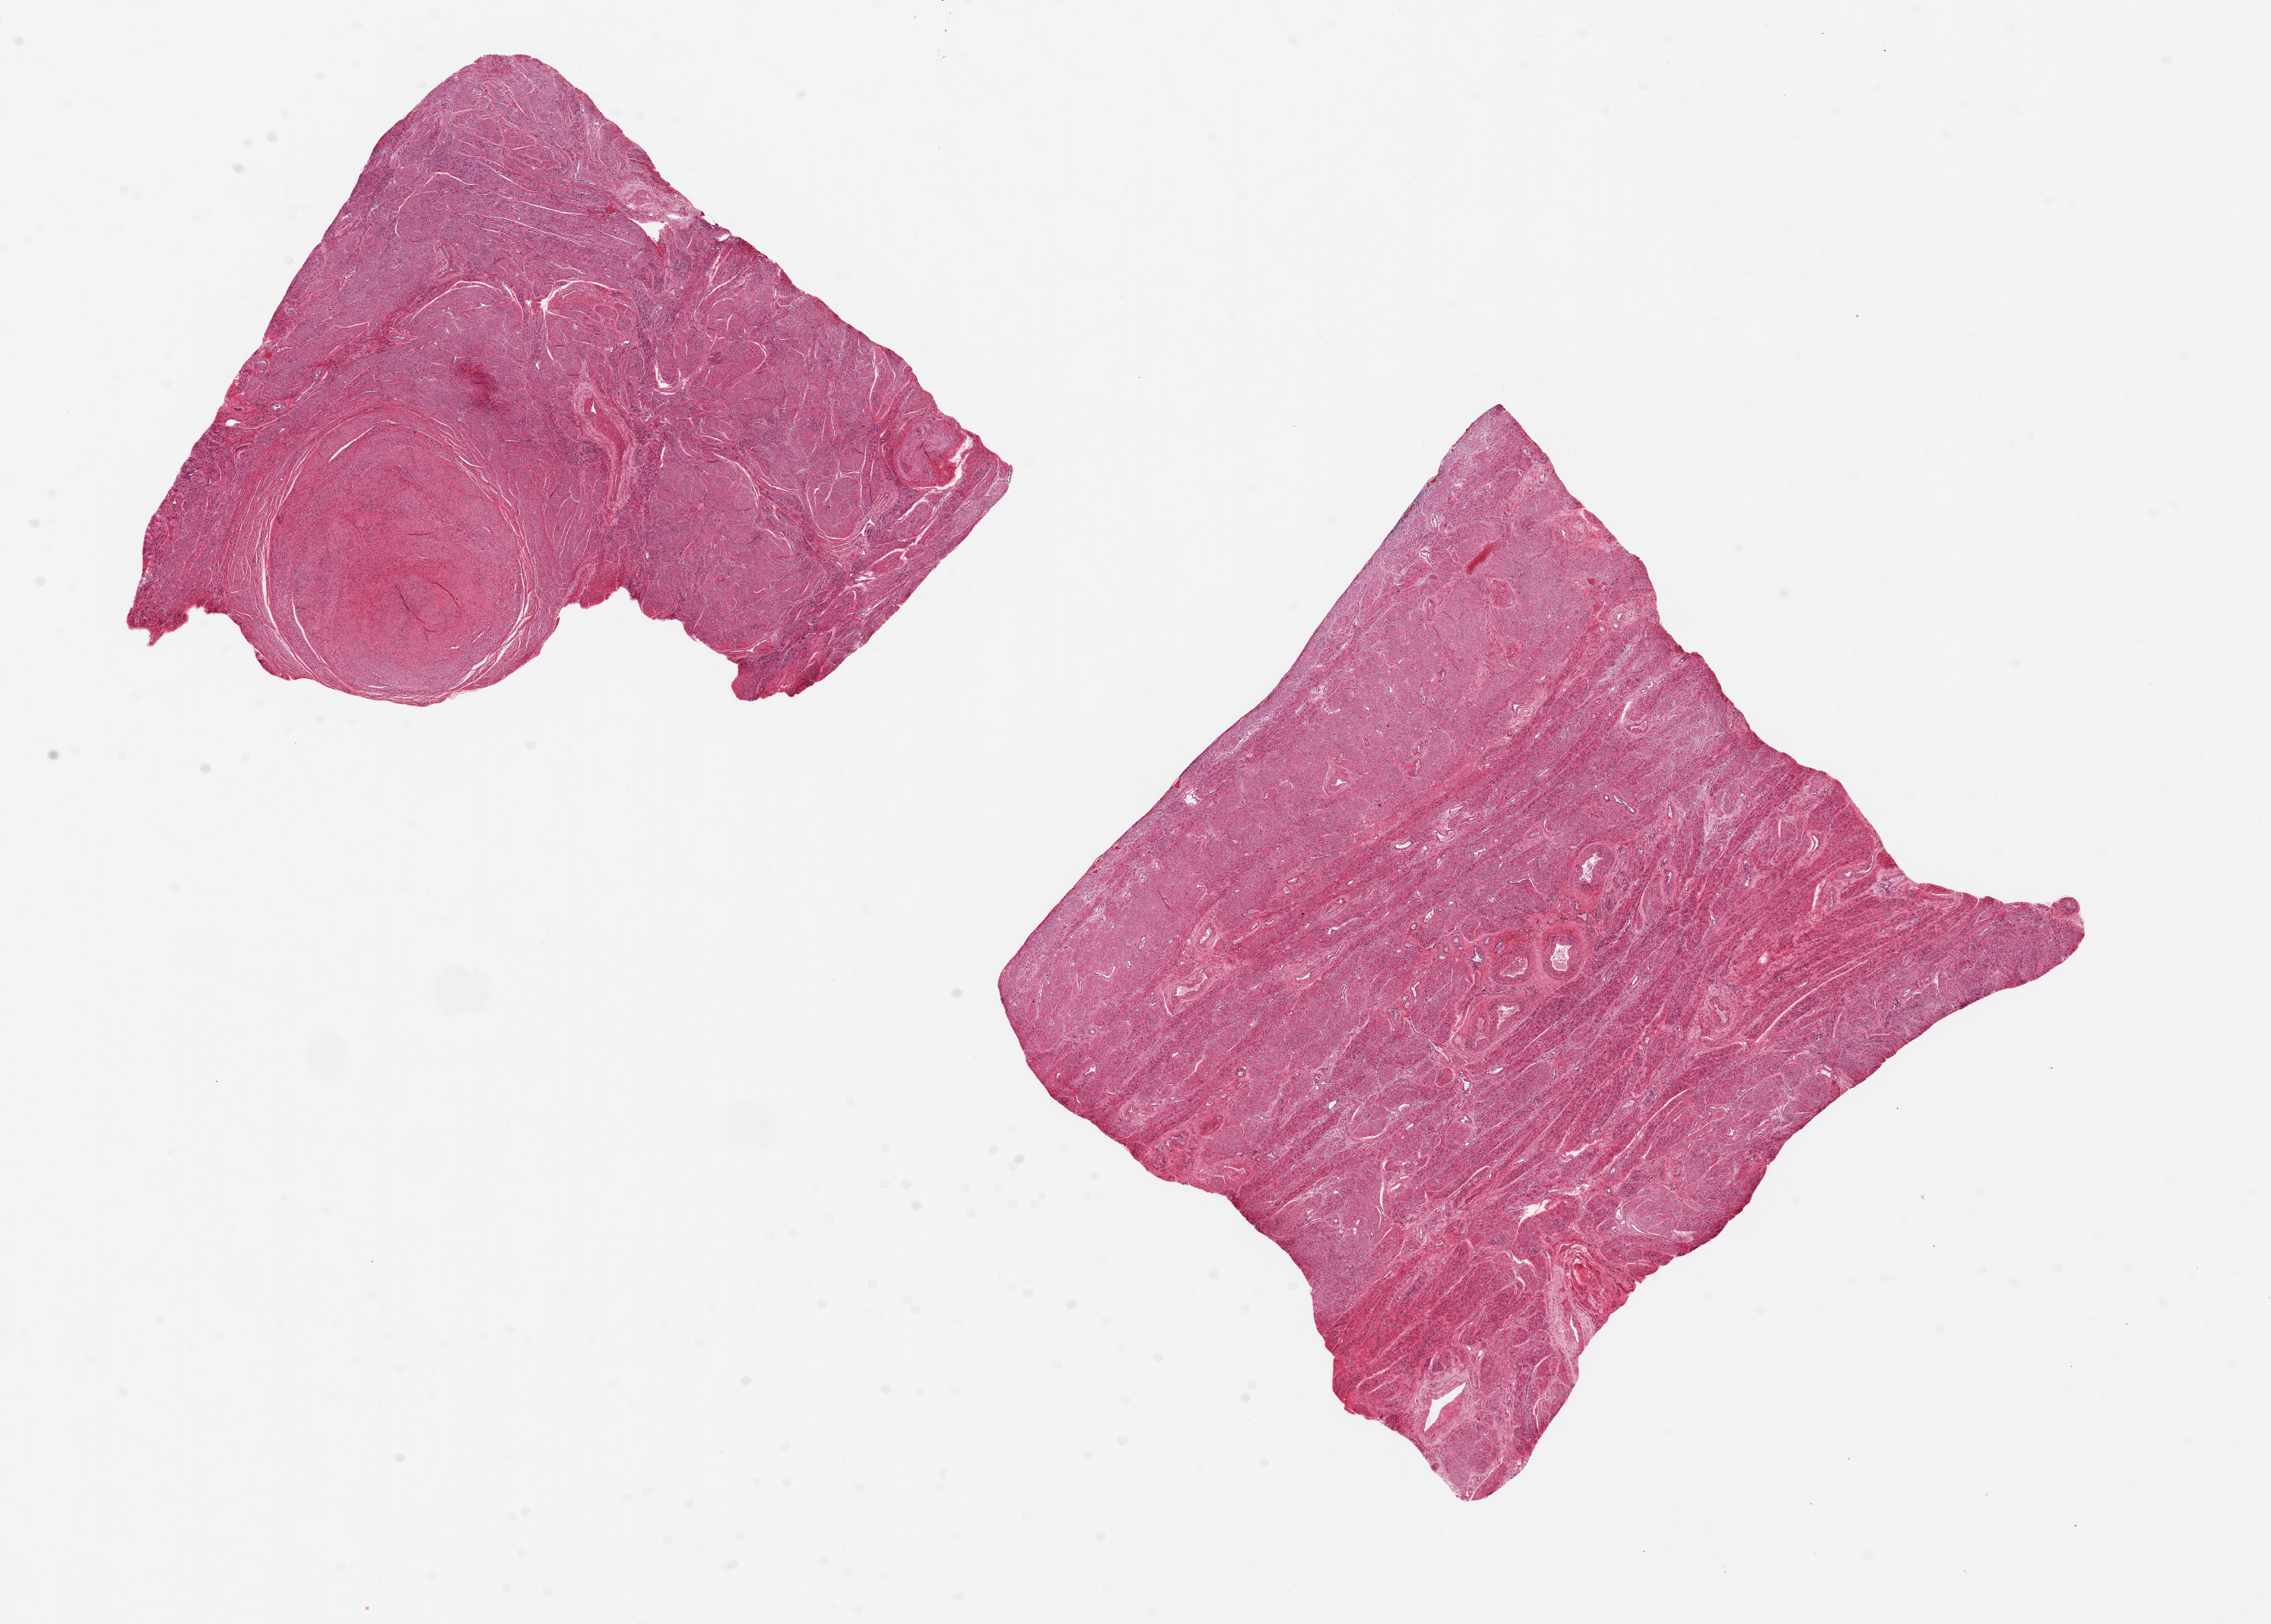
Hematoxylin and eosin (H&E) whole-slide image — whole scanned area (about 23.6 x 16.9 mm) shown as a low-resolution overview. PAXgene-fixed paraffin-embedded (PFPE) section. Section of uterus (target tissue). Tissue donor sample. Female donor.
* pathologist's review note for this sample: 2 pieces ~8x7mm; No endometrium; all muscularis; incidental ~2.5mm leiomyoma present, in one aliquot